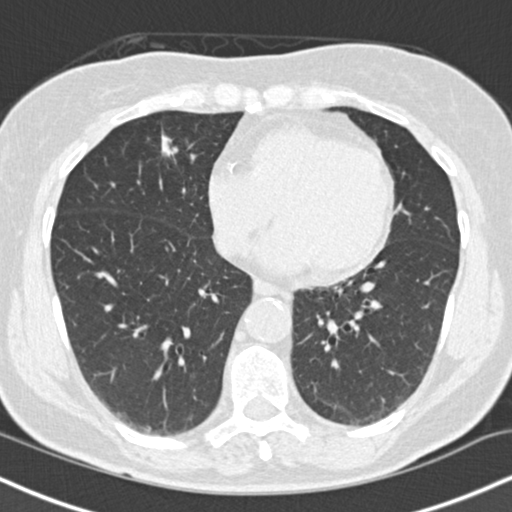
Low-dose screening chest CT, one axial slice. Position 57 of 145 along the scan axis. Reconstruction kernel B30f. 120 kVp. Lung window (W 1500 / L -600 HU). 2 mm slice thickness. 512 × 512 image matrix.
Outlined on this slice (outlined manually by an expert reader):
- lesion 1 (tumor, middle lobe of right lung): bounding box (x1, y1, x2, y2) in pixels: (161, 135, 178, 157)